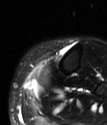
MRI of an extremity soft-tissue mass, one axial slice; slice 19 of 78 in the series (ordered by position); T2-weighted fat-saturated; MR volume resampled by the dataset authors to the PET/CT grid (not the native acquisition matrix); 107 × 125 image matrix. Female patient. Case-level facts recorded for this patient, not image findings: histological type: extraskeletal high grade osteogenic sarcoma; grade: high; site of the primary tumour: left calf.
Outlined on this slice (expert contour drawn on MRI and transferred to this co-registered scan by the dataset authors):
- gross tumour volume (mass): box from (x=30, y=68) to (x=50, y=85) px